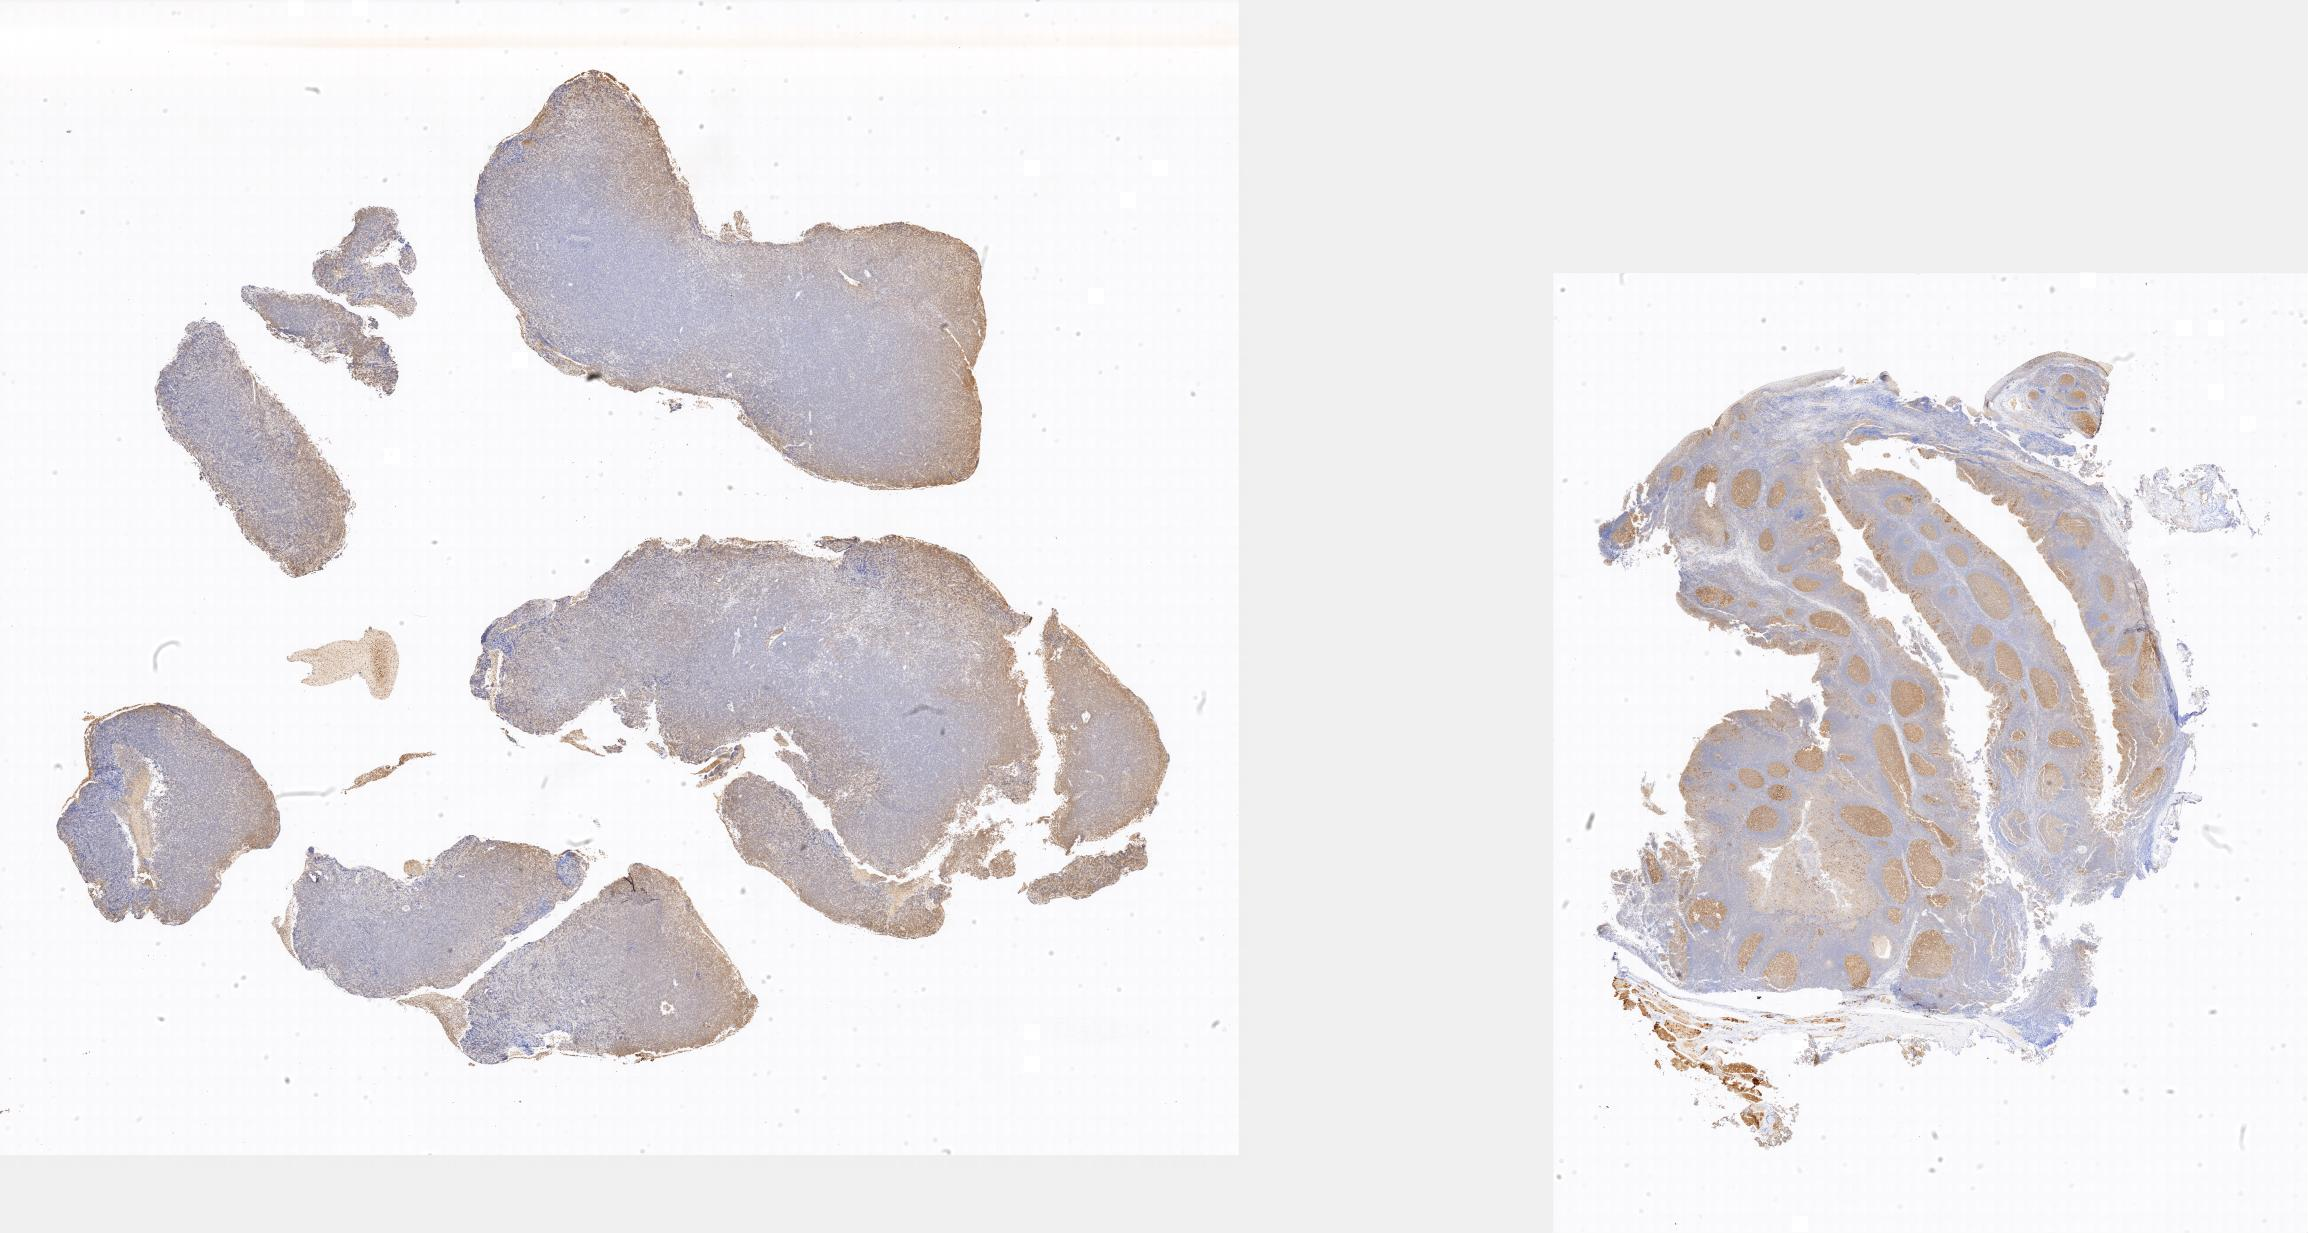
IHC for BCL6, whole-slide image, low-resolution overview of the scanned area, specimen: tumor tissue, site: soft tissue. Female, age 9 years at initial diagnosis.
* diagnosis: Burkitt lymphoma, NOS